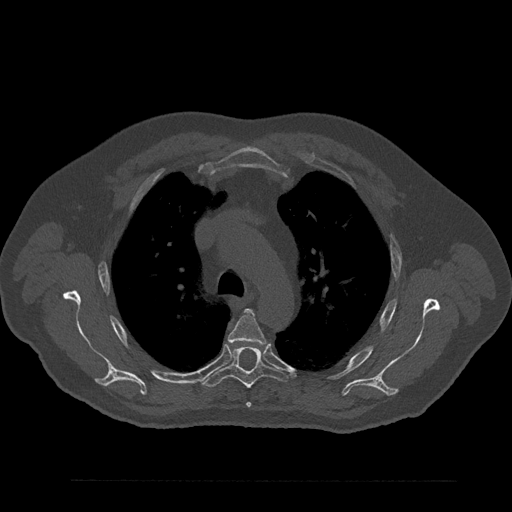
CT including the spine, one axial slice; position 617 of 797 along the scan axis; 120 kVp; bone window (W 1800 / L 400 HU); 512 × 512 image matrix. Patient: male, 61 years. Case-level facts recorded for this patient, not image findings: primary cancer: prostate.
Outlined on this slice (semi-automatically segmented with operator editing):
- T4 vertebra: bounding box (x1, y1, x2, y2) in pixels: (227, 309, 266, 408)
- T5 vertebra: (202, 347, 288, 389)